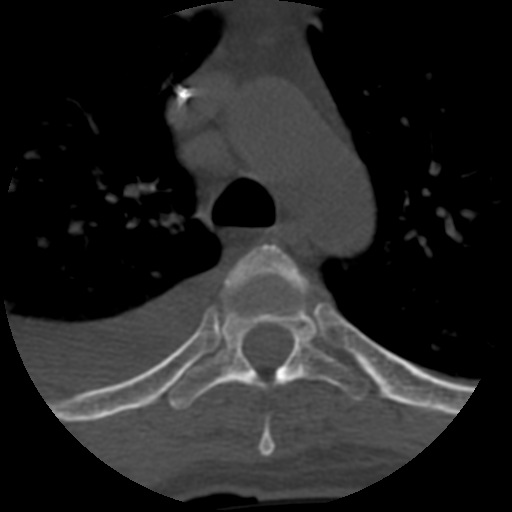
CT including the spine, one axial slice. Slice 460 of 708 in the series (ordered by position). 120 kVp. One of 3 acquisitions stored at this slice position. Bone window (W 1800 / L 400 HU). 1.25 mm slice thickness. 512 × 512 image matrix. Patient age 55 years. Case-level facts recorded for this patient, not image findings: primary cancer: colon; vertebrae with lytic lesions (as recorded): T12, L1, L5.
Structures marked on this image (semi-automatically segmented with operator editing):
- T4 vertebra: box from (x=220, y=239) to (x=309, y=457) px
- T5 vertebra: (x=168, y=297)–(x=371, y=411)